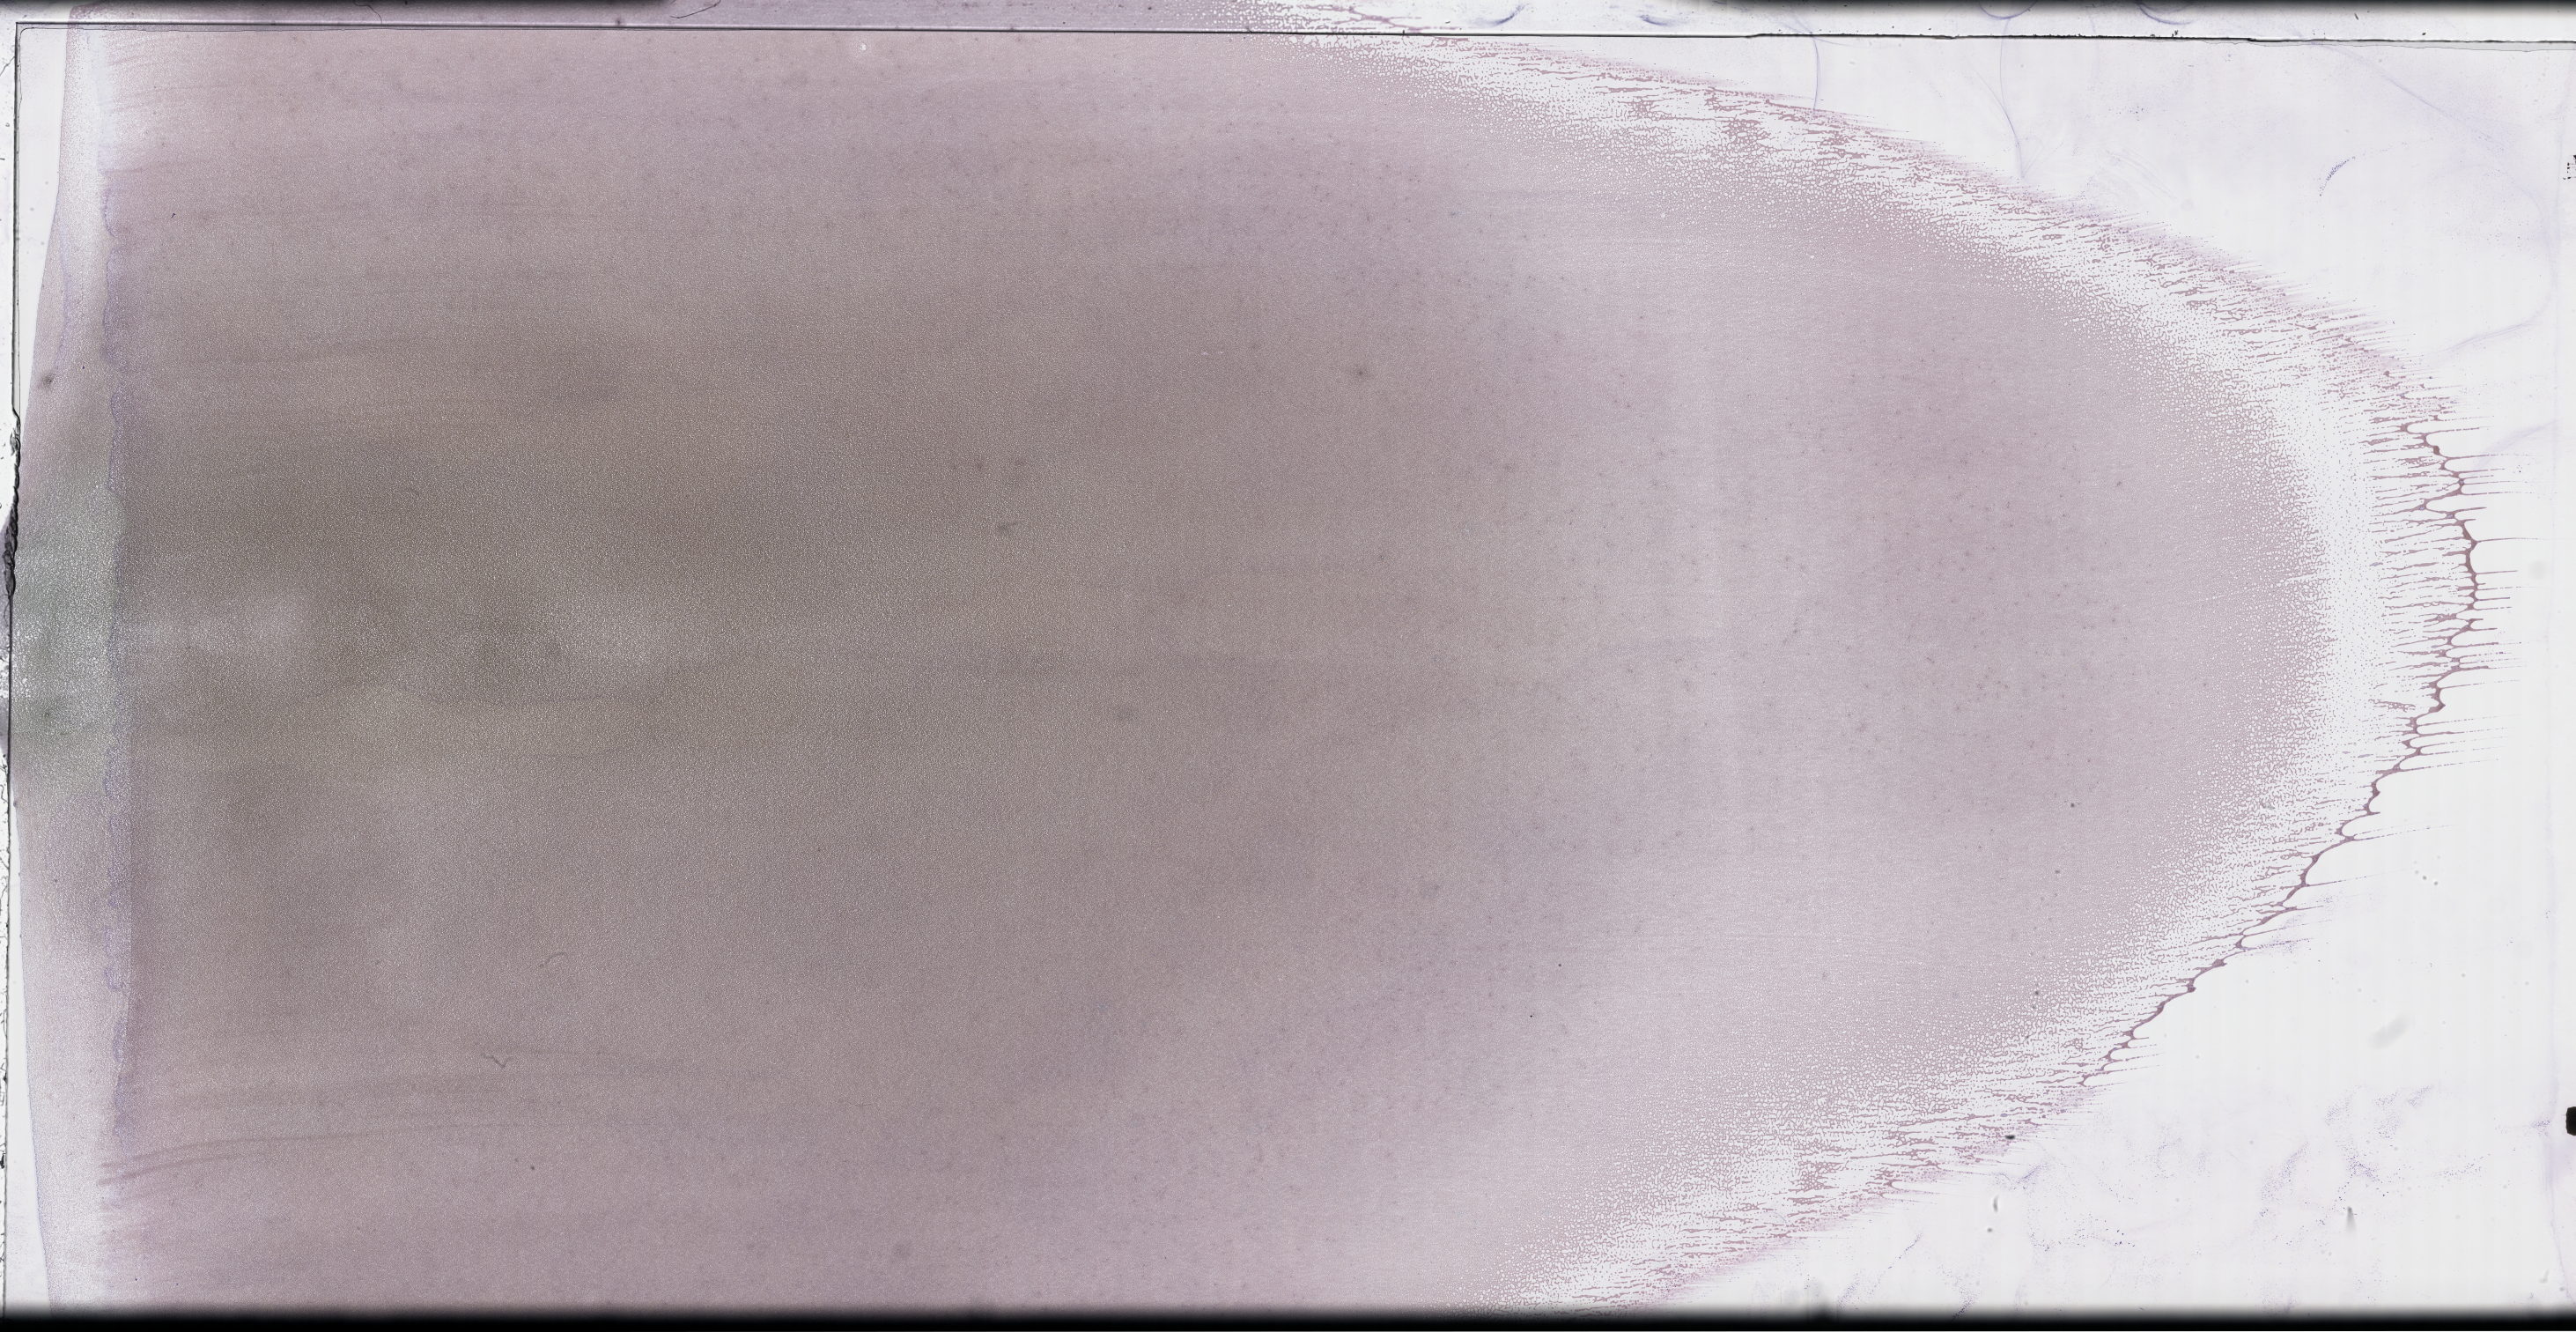
Whole-slide image of a whole blood smear, Wright–Giemsa stain, a low-resolution overview of the entire scanned area, about 47.2 x 24.4 mm; collected on treatment. Male patient.
* from a patient with: Plasma Cell Myeloma